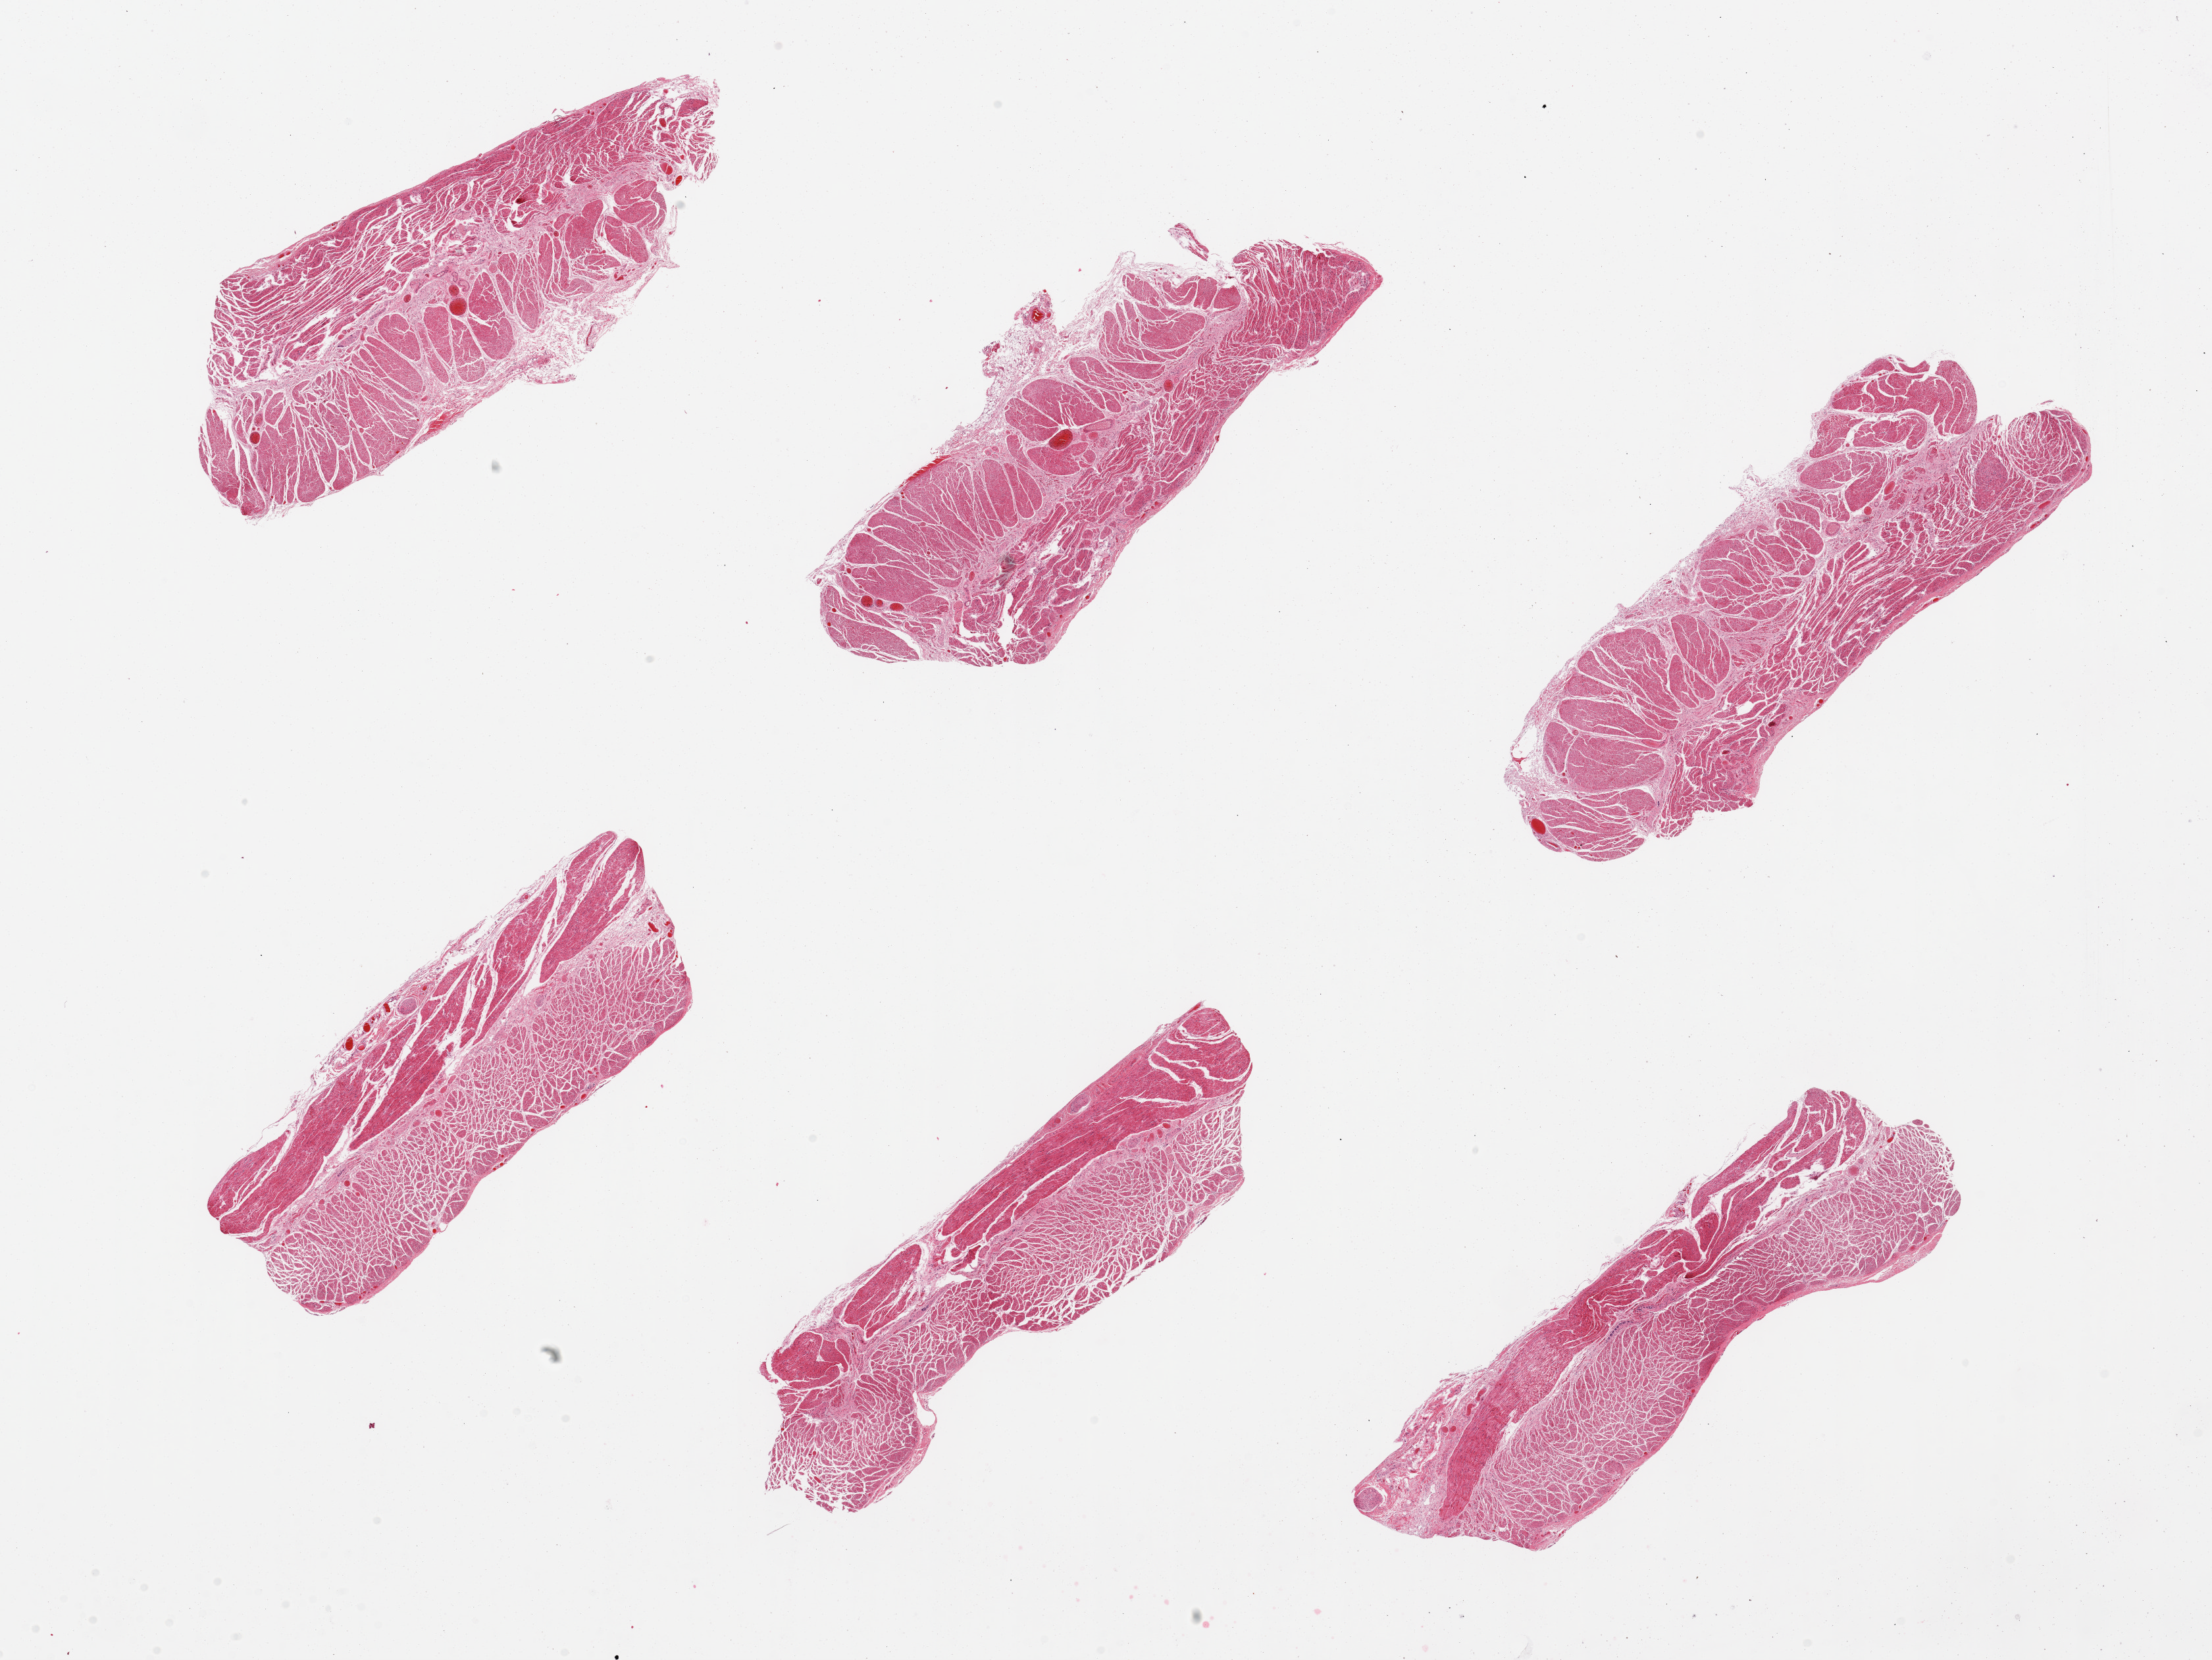
H&E whole-slide image, brightfield, a low-resolution overview of the entire scanned area, about 26.6 x 19.9 mm. PAXgene-fixed, paraffin-embedded tissue. Section of esophageal muscle (target tissue). Tissue donor sample. Donor sex: male.
* reviewer comment on this tissue sample: 6 pieces, all target muscularis